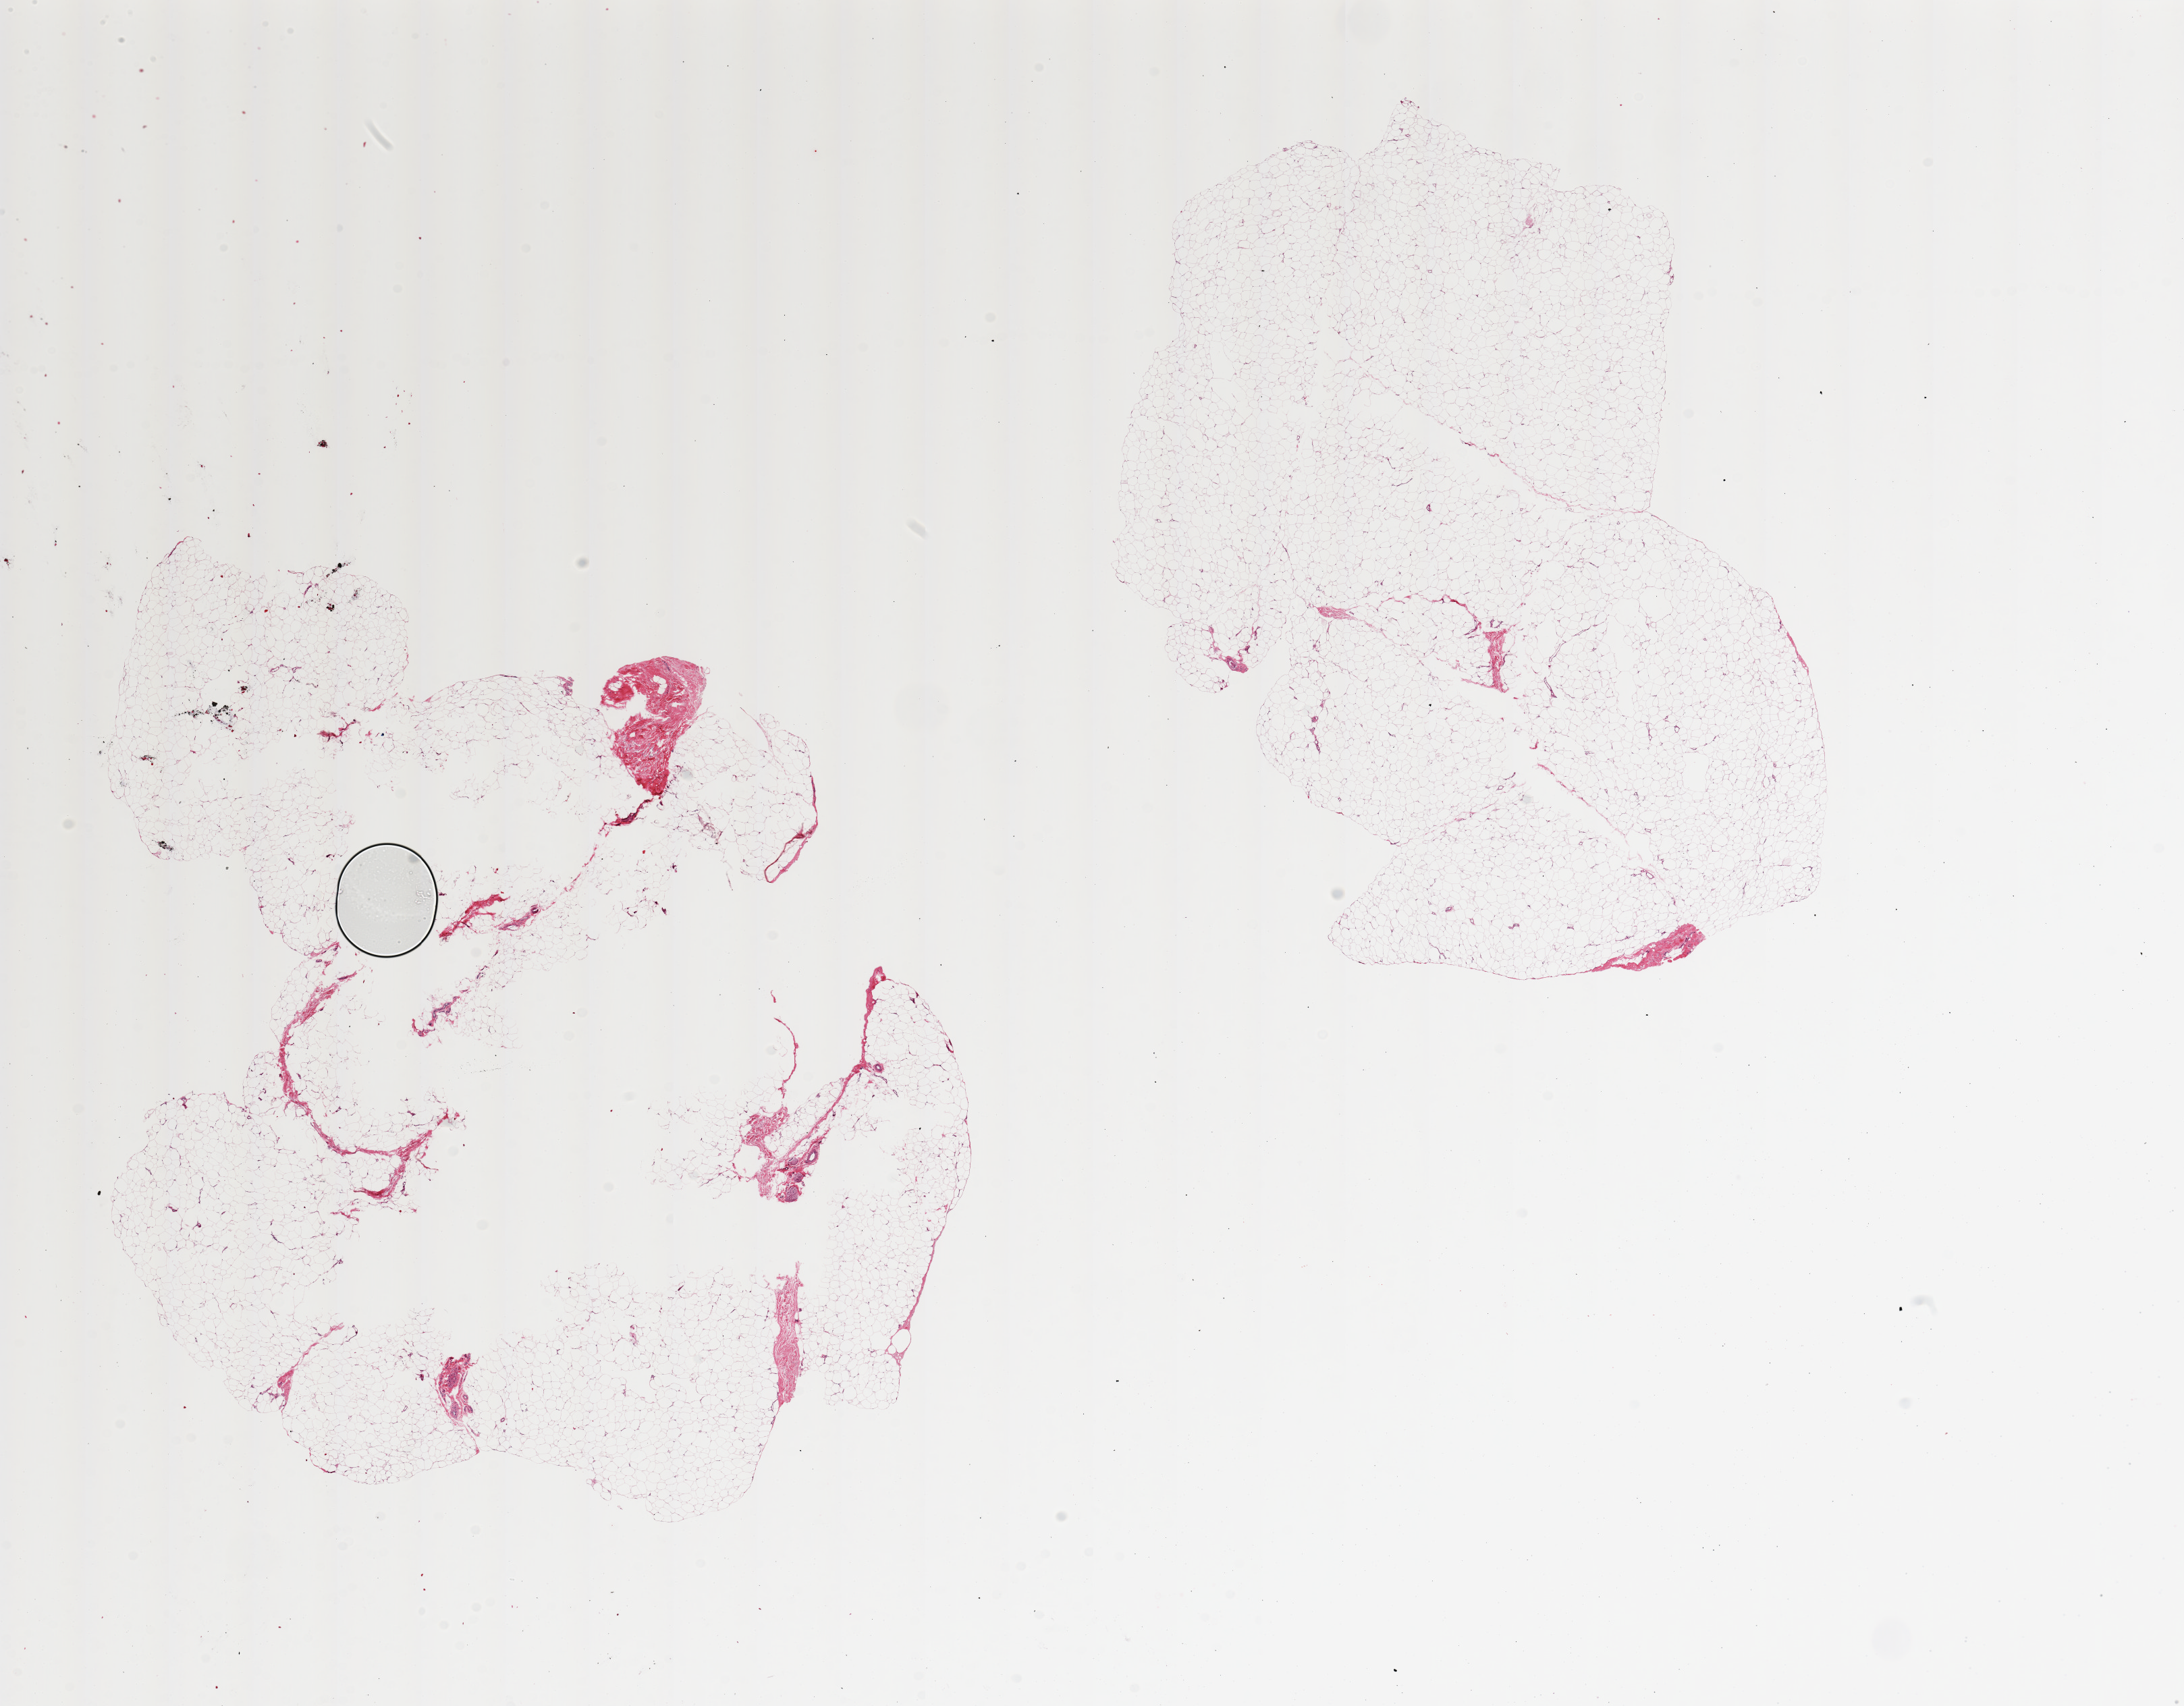
Whole-slide image, H&E stain, brightfield, a low-resolution overview of the entire scanned area, about 25.6 x 20.0 mm, PAXgene-fixed paraffin-embedded (PFPE) section, sampled site (target tissue): adipose tissue, tissue donor sample. Female donor.
• review note (as recorded): 2 pieces, 13x10 & 10x8mm